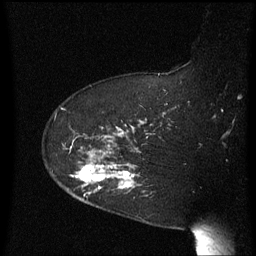
Breast MRI (dynamic contrast-enhanced), one sagittal slice; slice 47 of 60 in the series (ordered by position); dynamic contrast-enhanced series, image 2 of 3 at this slice position (ordered by acquisition); 1.5 T; TE 4.2 ms, TR 8.4 ms; 2.3 mm slice thickness; 256 × 256 image matrix, field of view 200 × 200 mm. Female patient, age 63 years. Case-level facts recorded for this patient, not image findings: setting: breast cancer imaged before/during neoadjuvant chemotherapy; receptor status: HER2-positive.
Structures marked on this image (semi-automatic segmentation, software-assisted and operator-edited):
- analysis volume of interest (the breast-tissue region the enhancement analysis was run in; not a lesion): bounding box <63,144,141,206> (left, top, right, bottom; pixels)
- tumour enhancement mask (voxels above the 70 % enhancement threshold inside the analysis volume of interest): <72,163,135,189>